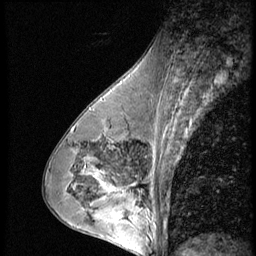
Breast MRI (dynamic contrast-enhanced), one sagittal slice. Slice 32 of 56 in the series (ordered by position). 3 images stored at this slice position (order not interpretable as contrast timing). 1.5 T. TE 4.2 ms, TR 9 ms. 2.5 mm slice thickness. 256 × 256 image matrix, field of view 180 × 180 mm. Female patient, age 43 years. From the clinical record (not read from this slice): setting: breast cancer imaged before/during neoadjuvant chemotherapy; receptor status: HR-positive, HER2-negative.
Annotated regions visible in this slice (semi-automatic segmentation, software-assisted and operator-edited):
- analysis volume of interest (the breast-tissue region the enhancement analysis was run in; not a lesion): bounding box <120,160,163,207> (left, top, right, bottom; pixels)
- tumour enhancement mask (voxels above the 140 % enhancement threshold inside the analysis volume of interest): <120,182,141,193>